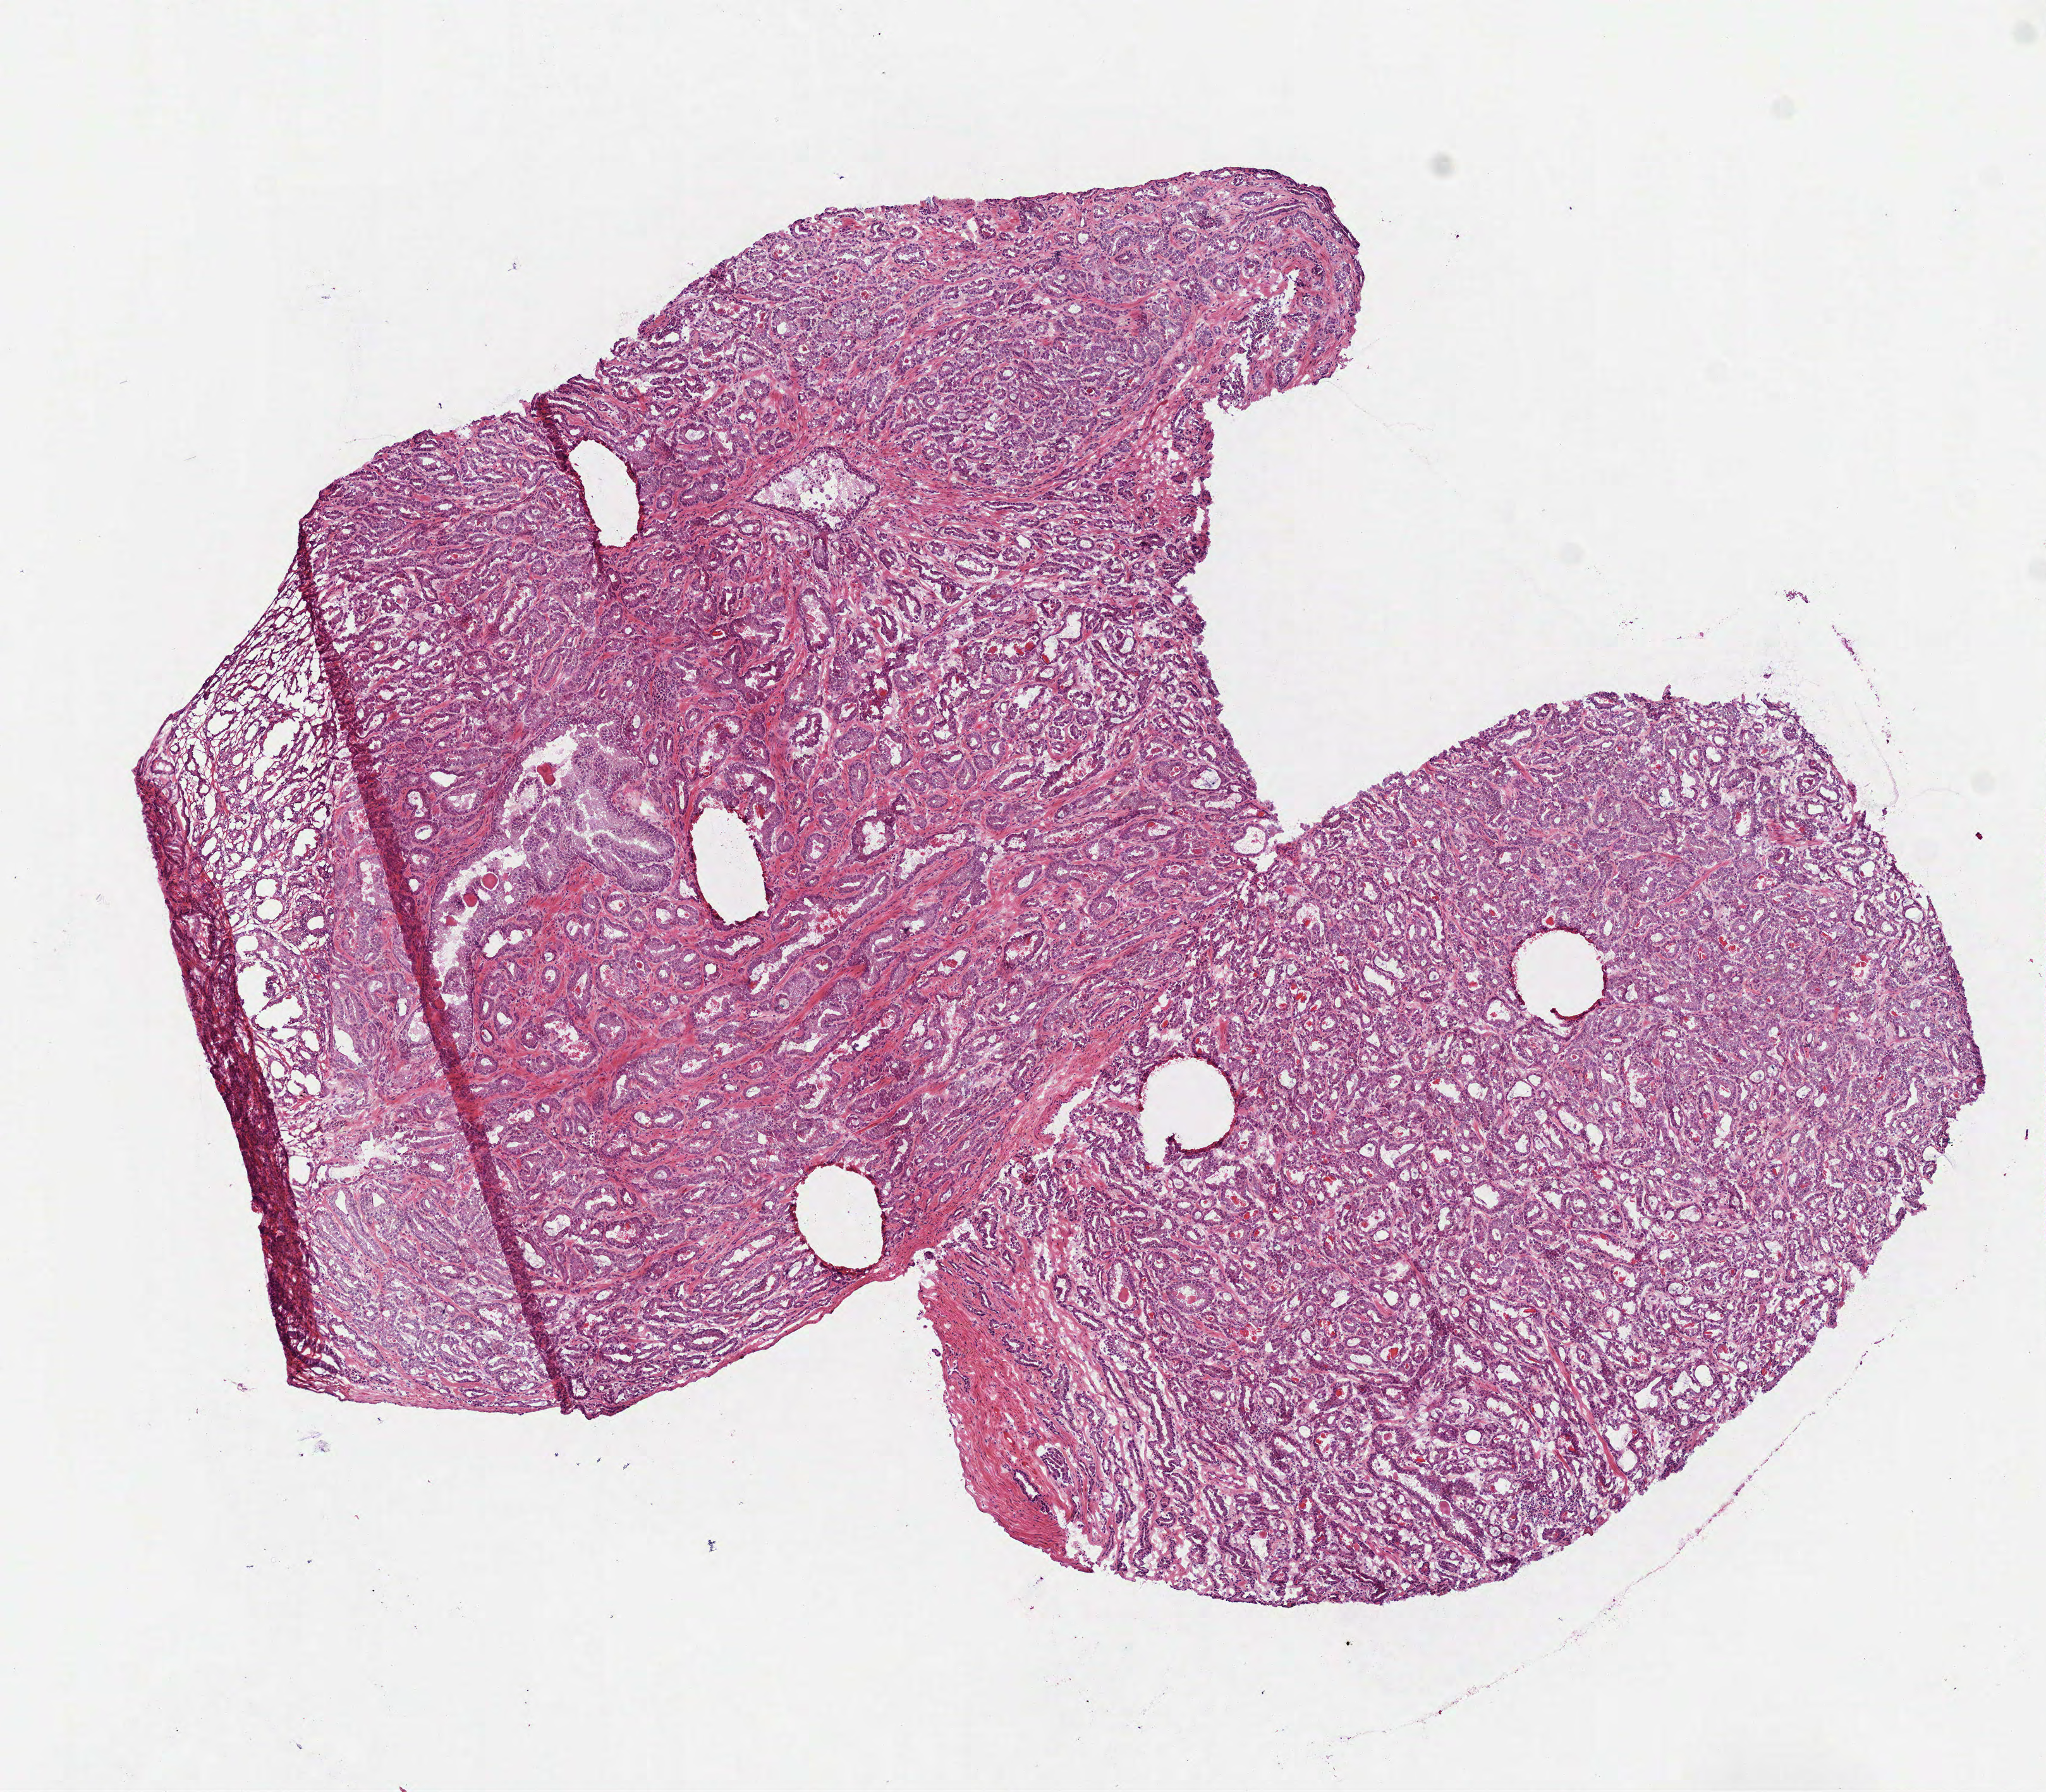
H&E-stained whole-slide image — low-resolution overview of the scanned area, about 6.5 x 5.7 mm (acquisition: 40x scan); frozen section from the top of the tissue portion; prostate, primary tumour sample. Male patient; age at initial diagnosis 63 years. Composition of this section per pathologist review: tumour cells 90%, tumour nuclei 85%.
Histologic diagnosis: Acinar cell carcinoma (prostate gland).